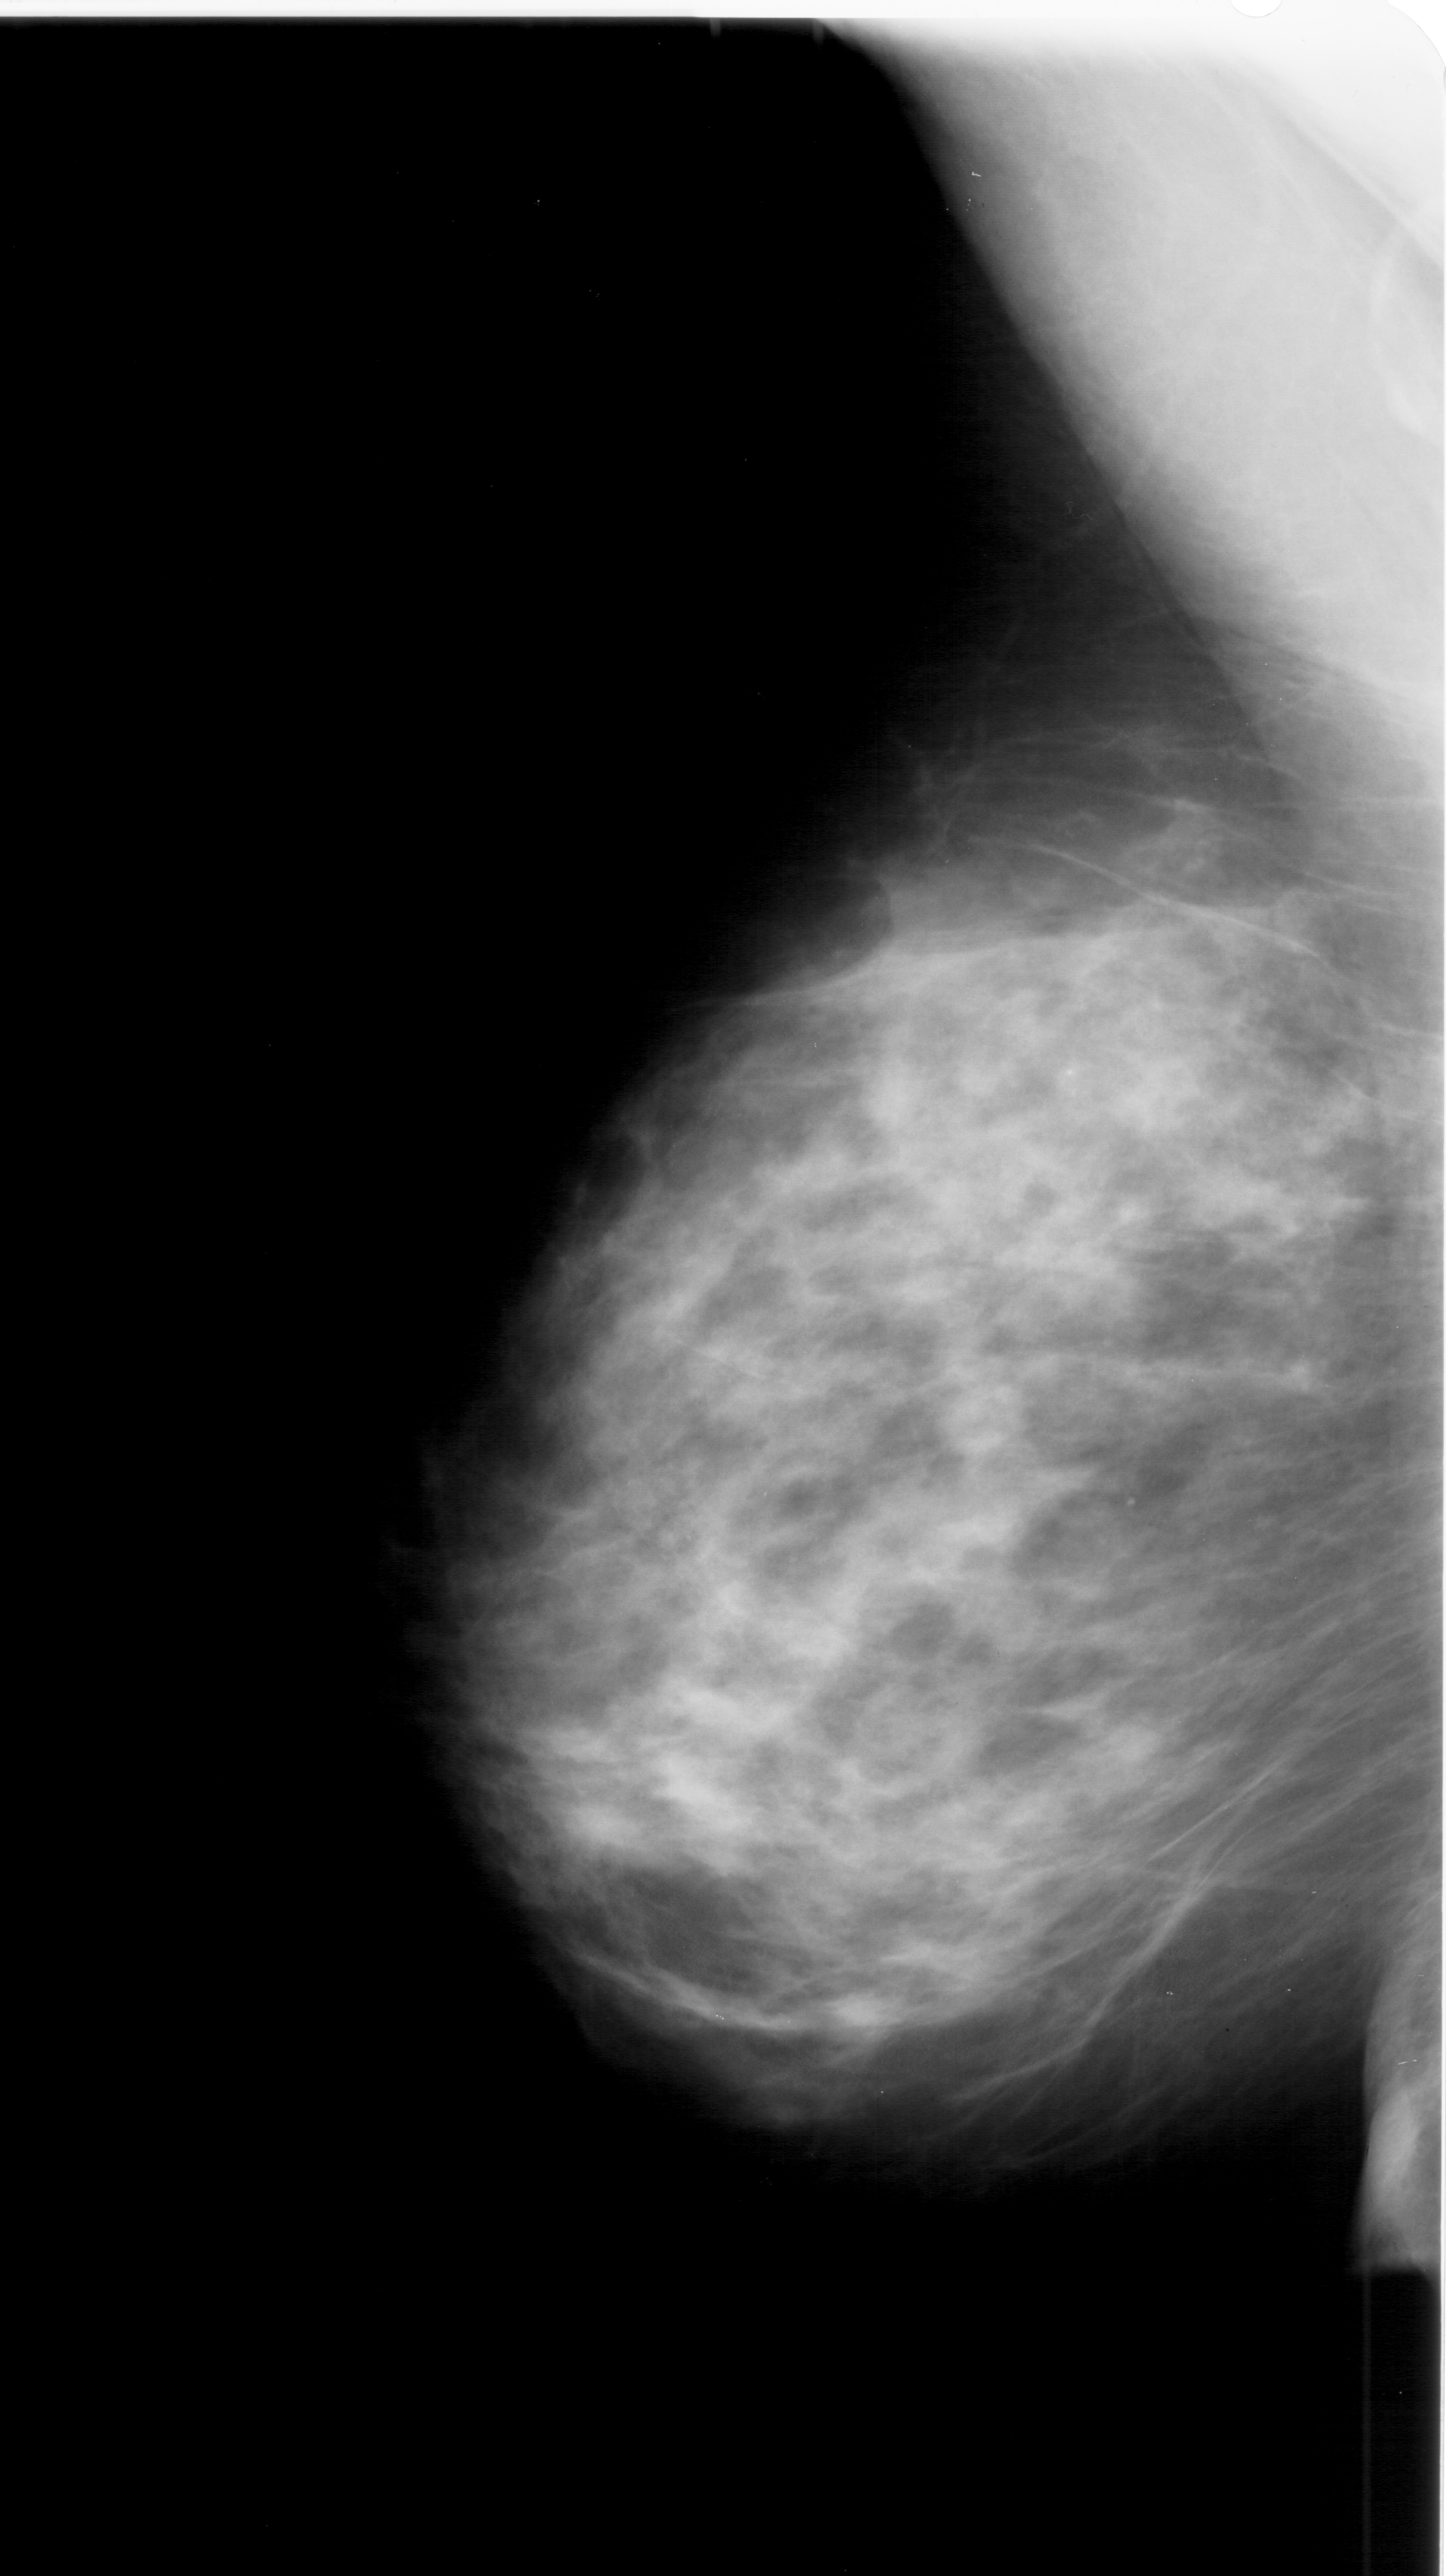
Digitized screen-film mammogram; left breast; MLO view; breast composition: extremely dense (BI-RADS density category 4 of 4); 1446 × 2576 image matrix.
Expert-marked regions of interest on this film, with their recorded descriptors:
- calcifications, morphology pleomorphic, distribution clustered; BI-RADS assessment category 4; pathology result (as recorded, not read from the image): benign: bounding box [x1, y1, x2, y2] px = [976, 1003, 1128, 1177]